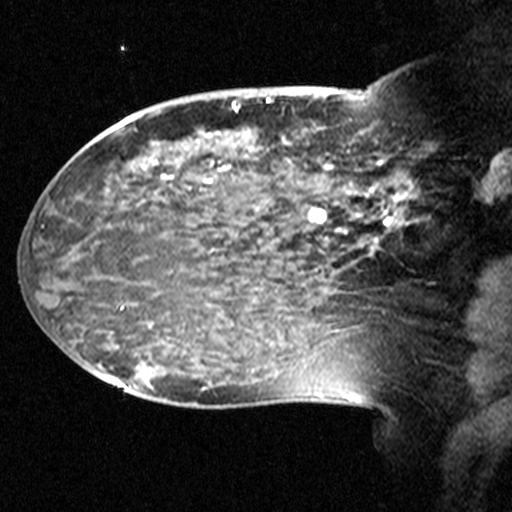
Breast MRI (dynamic contrast-enhanced), one sagittal slice; slice 17 of 44 in the series (ordered by position); dynamic contrast-enhanced study with each time point stored as its own series, time point 2 of 3 at this slice position (early post-contrast, ordered by acquisition time); 1.5 T; TE 4.5 ms, TR 11 ms; 512 × 512 image matrix, field of view 240 × 240 mm. Patient: female, 38 years. Case-level facts recorded for this patient, not image findings: setting: breast cancer imaged before/during neoadjuvant chemotherapy; receptor status: HR-positive, HER2-negative.
Outlined on this slice (semi-automatically segmented with operator editing):
- analysis volume of interest (the breast-tissue region the enhancement analysis was run in; not a lesion): bounding box <124,106,405,245> (left, top, right, bottom; pixels)
- tumour enhancement mask (voxels above the 90 % enhancement threshold inside the analysis volume of interest): <162,107,390,231>